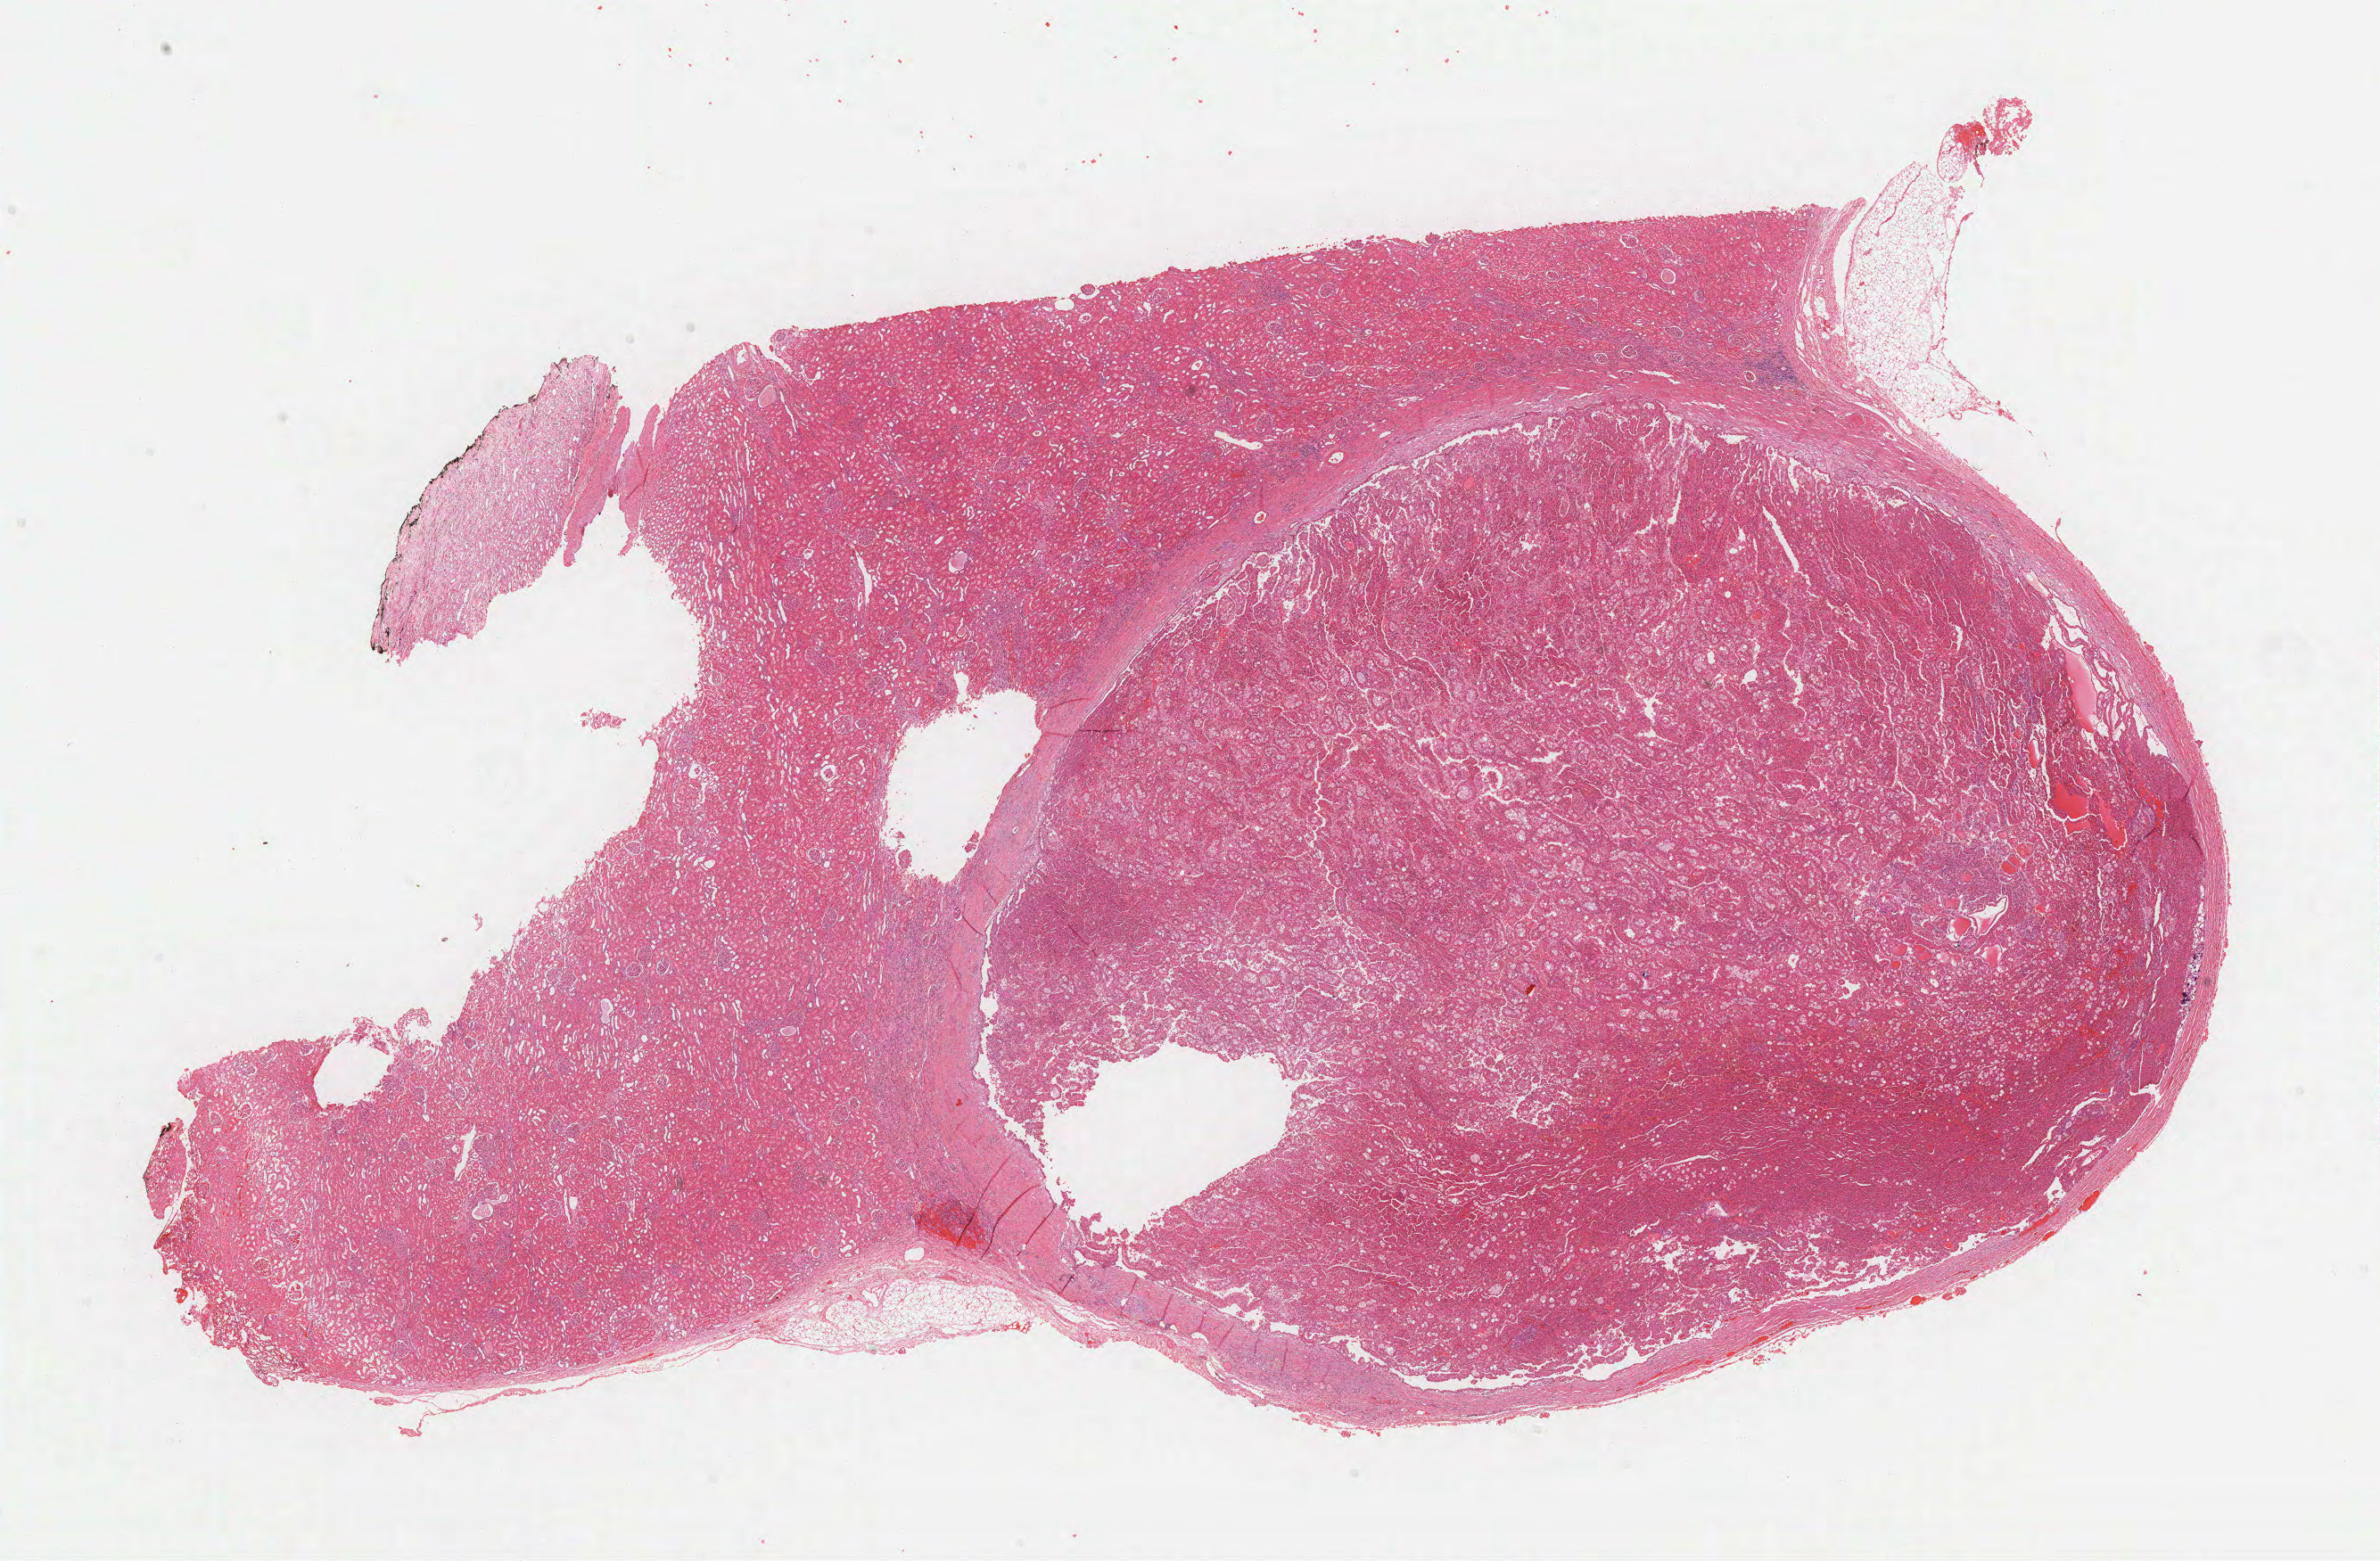
Digitized Hematoxylin and eosin (H&E) stained tissue section (whole slide) — shown as a low-resolution overview of the whole scanned area (about 21.6 x 14.1 mm). Formalin-fixed paraffin-embedded (FFPE) diagnostic section. Sample: primary tumour, kidney. Male, age 63 years at initial diagnosis.
• AJCC pathologic stage: I (7th edition)
• diagnosis: Papillary adenocarcinoma, NOS
• laterality: left